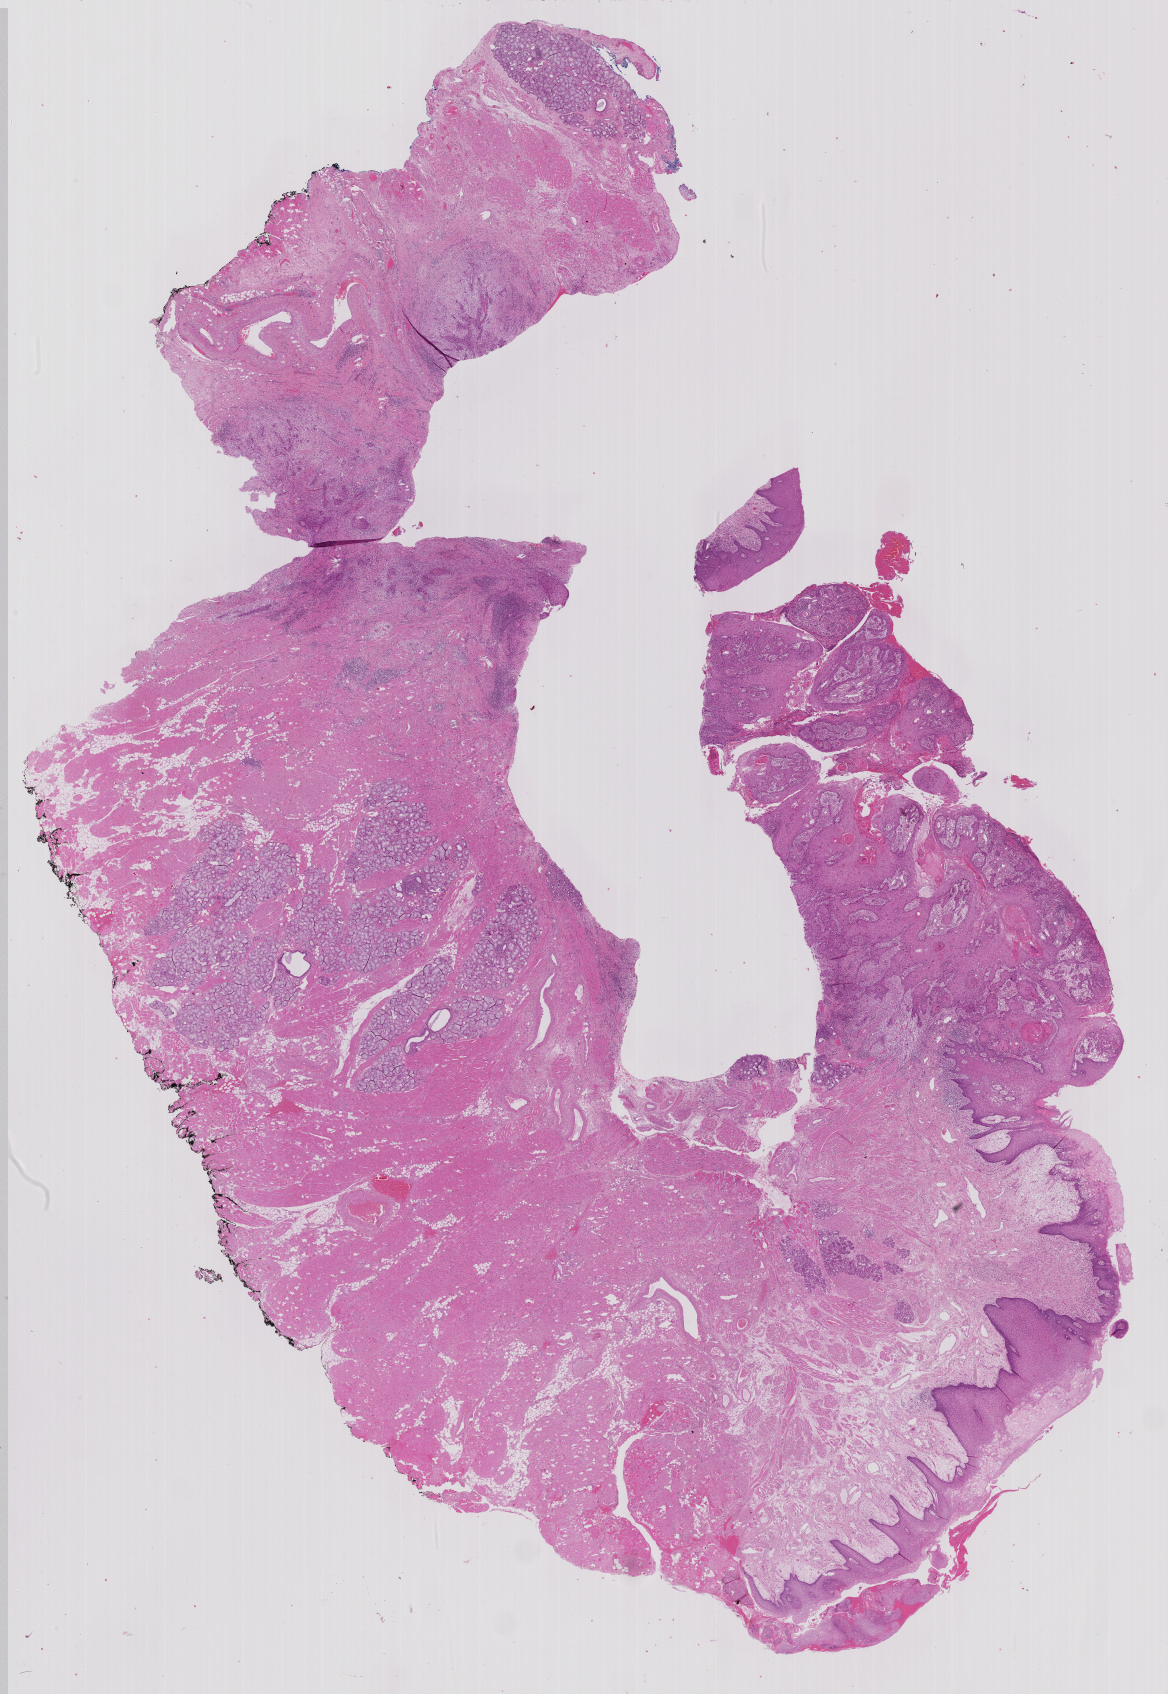
Hematoxylin and eosin (H&E) stained whole-slide image, low-resolution overview of the scanned area, about 18.7 x 27.1 mm (from a 40x scan); formalin-fixed paraffin-embedded (FFPE) diagnostic section; primary tumour sample from the head and neck. Male, age 69 years at initial diagnosis. Histologic grade: G3 (poorly differentiated).
* laterality: right
* AJCC pathologic stage: II (7th edition)
* pathologic diagnosis: Squamous cell carcinoma, keratinizing, NOS